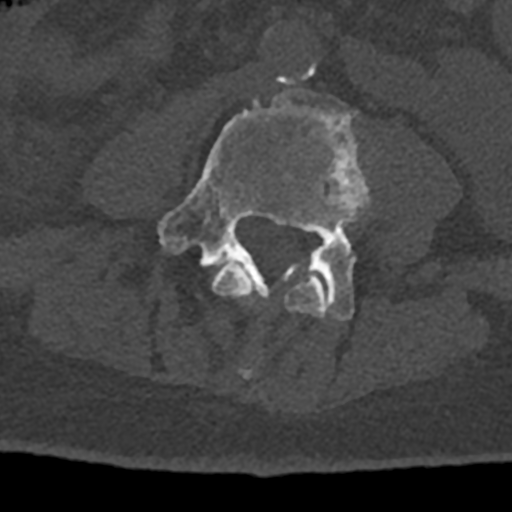
CT including the spine, one axial slice. Slice 273 of 797 in the series (ordered by position). Reconstruction kernel Br40s/3. 120 kVp. Bone window (W 1800 / L 400 HU). 512 × 512 image matrix, field of view 160 × 160 mm. Male patient, age 74 years. From the clinical record (not read from this slice): primary cancer: renal; vertebrae with lytic lesions (as recorded): T10, L1, L2, L3, L4, L5.
Outlined on this slice (semi-automatically segmented with operator editing):
- L3 vertebra: bounding box (x1, y1, x2, y2) in pixels: (212, 261, 327, 378)
- L4 vertebra: (158, 86, 370, 321)